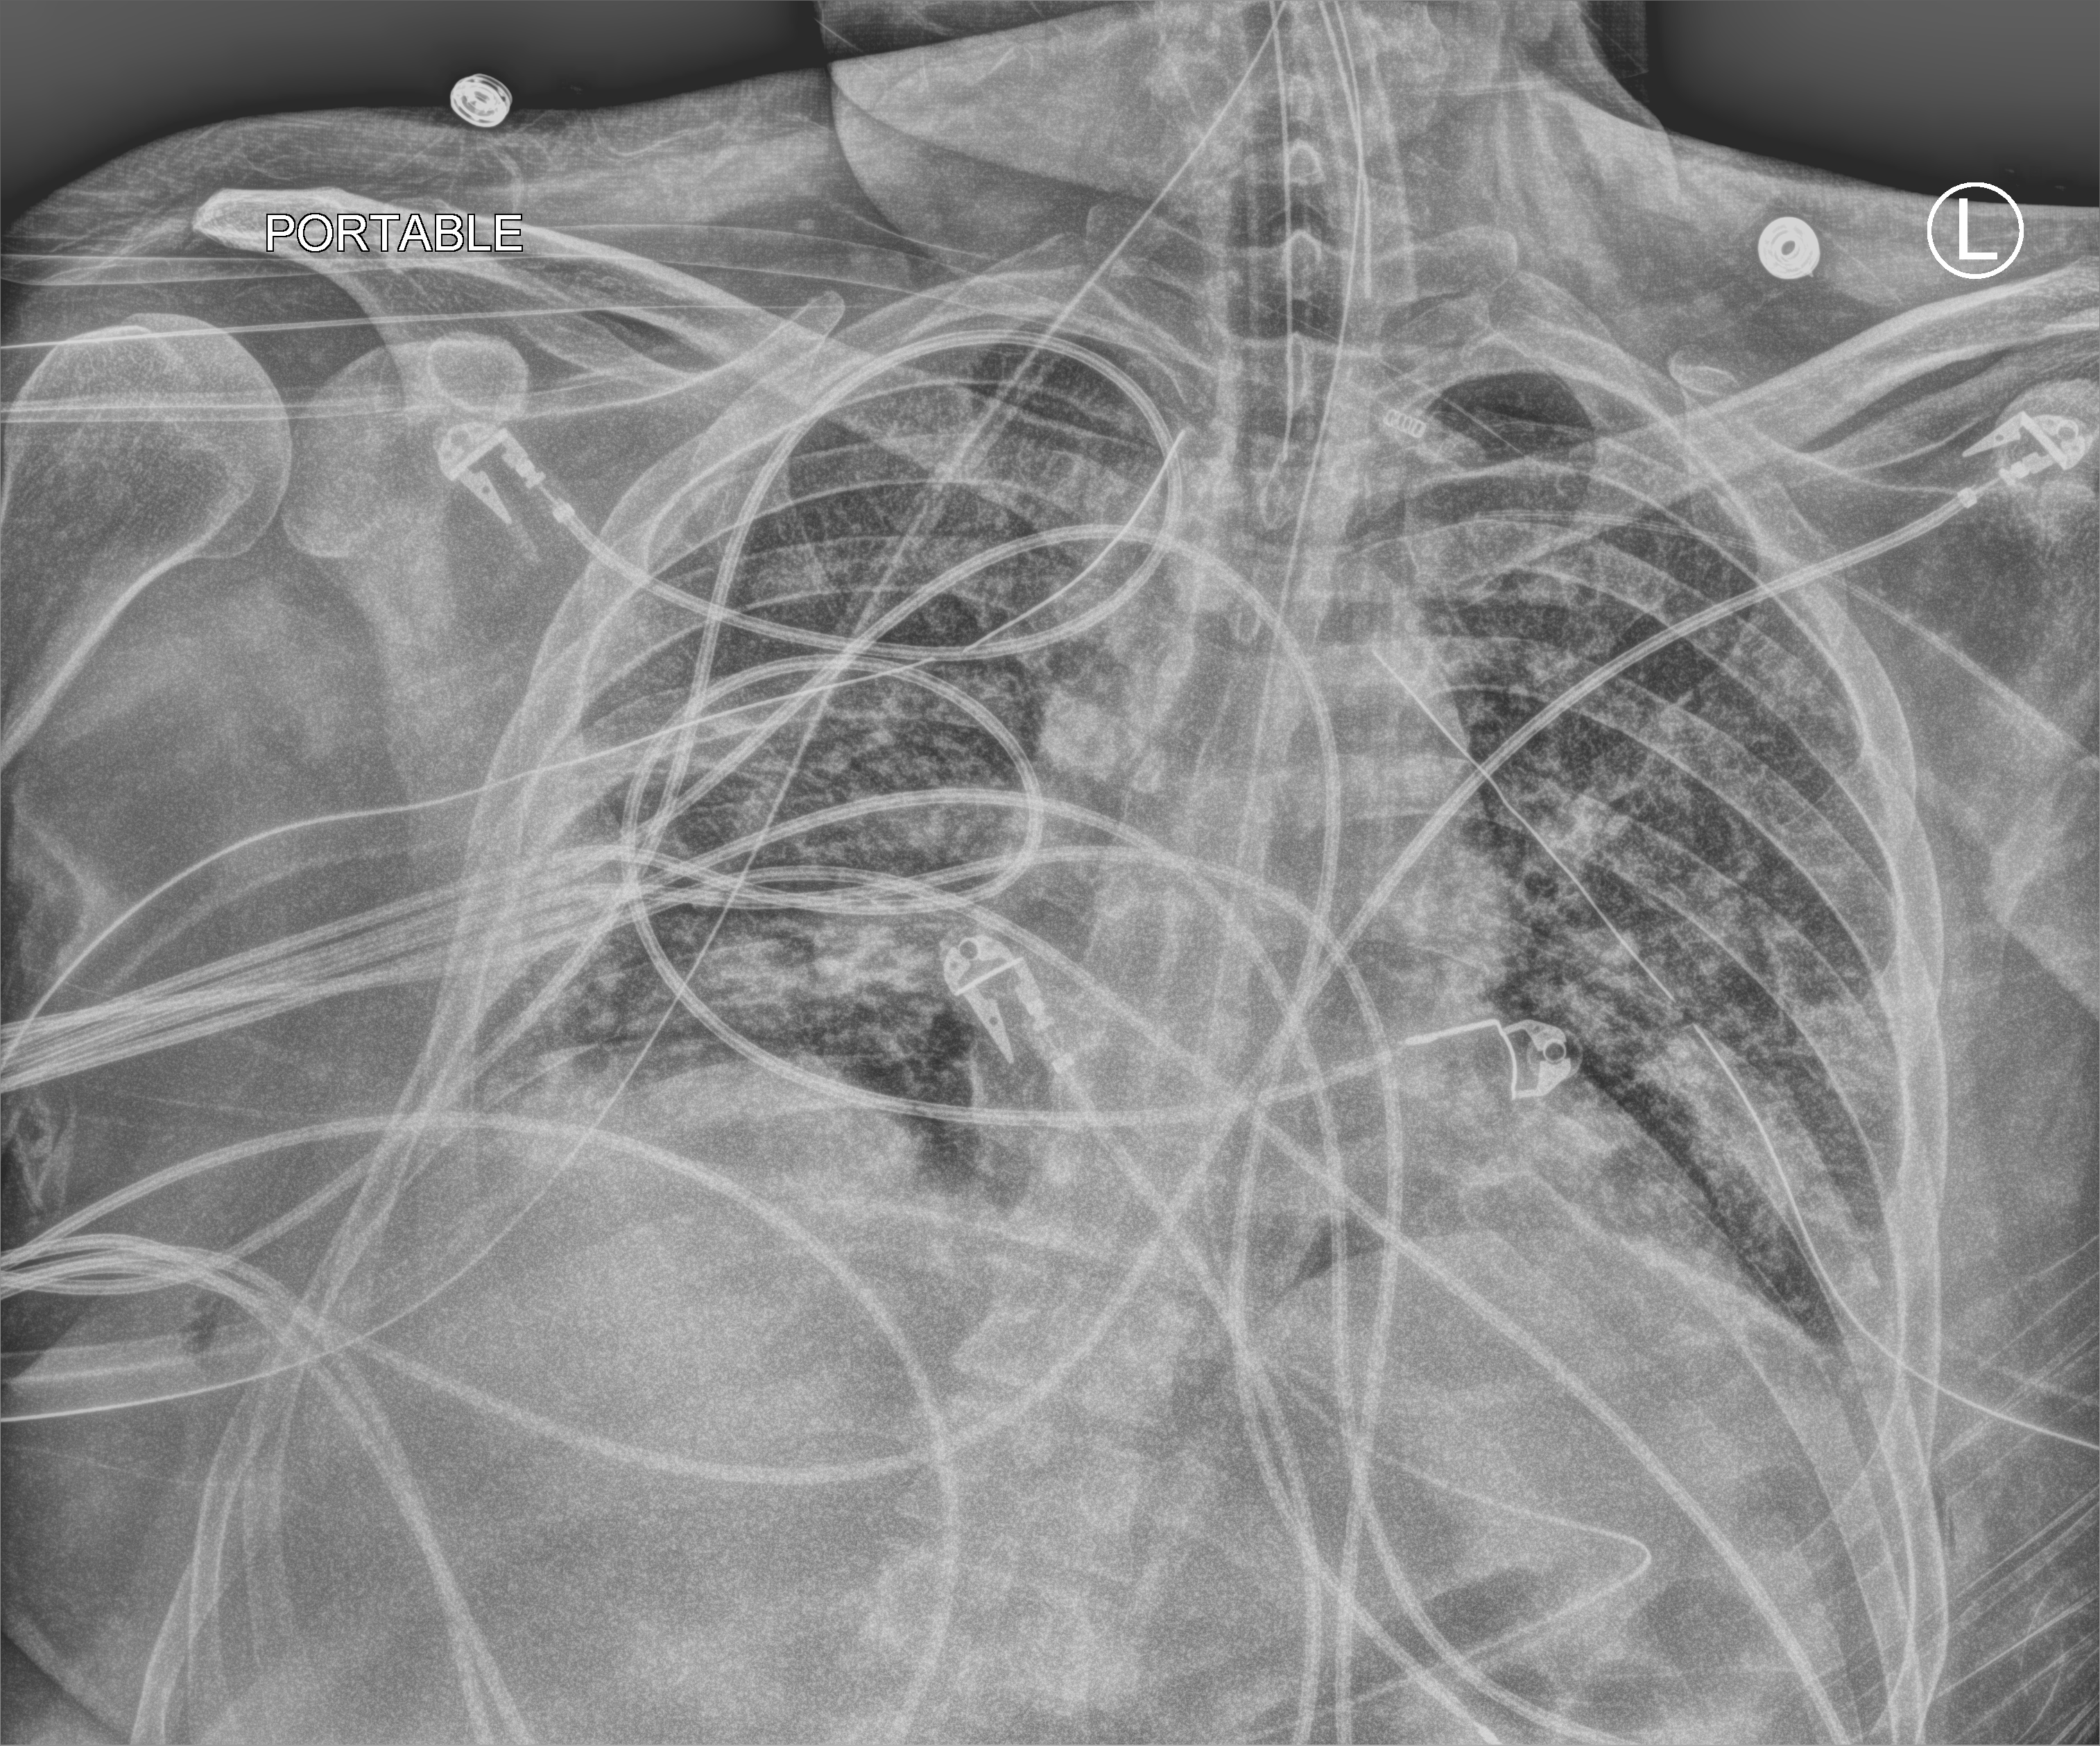
Bedside chest radiograph (computed radiography), anteroposterior (AP) projection. Patient hospitalised with COVID-19; male, aged 18–59 years.
Admission-level facts for this patient (not findings on this image; timing relative to this image not recorded): admitted to intensive care during this hospital stay: yes; mechanically ventilated during this hospital stay: yes.